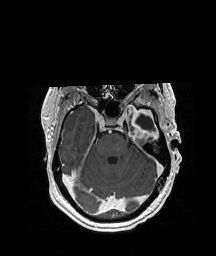
Brain MRI from a brain-tumour surgery series, one axial slice; position 138 of 208 along the scan axis; T1-weighted post-contrast; 1 mm slice thickness; 216 × 256 image matrix, field of view 228 × 270 mm. Case-level facts recorded for this patient, not image findings: histopathology: Glioblastoma; WHO grade: 4; IDH mutation: no; tumour location: Left Anterior/Superior Temporal.
Annotated regions visible in this slice (manually delineated by an expert):
- previous resection cavity: box from (x=135, y=114) to (x=156, y=132) px
- tumour: (x=125, y=100)–(x=158, y=138)